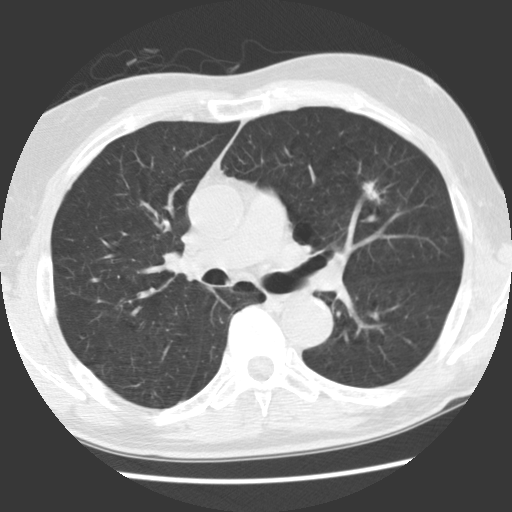
Axial slice from a low-dose chest CT screening exam; first (baseline) screen; lung window (W 1500 / L -600 HU); 2.5 mm slice thickness; standard (soft-tissue) reconstruction kernel (STANDARD). Male, age 70 years at enrolment. Current smoker at enrolment.
Expert reader's lesion annotation, box from (x=344, y=173) to (x=400, y=221) px. The screening reader recorded 2 non-calcified nodules or masses ≥4 mm on this exam (left upper lobe, right lower lobe); which of them this box marks is not recorded. Participant outcome: lung cancer diagnosed 879 days after this screen — adenocarcinoma, NOS, left upper lobe, moderately differentiated (G2), stage IIIA (AJCC 6th edition), 17 mm at pathology.